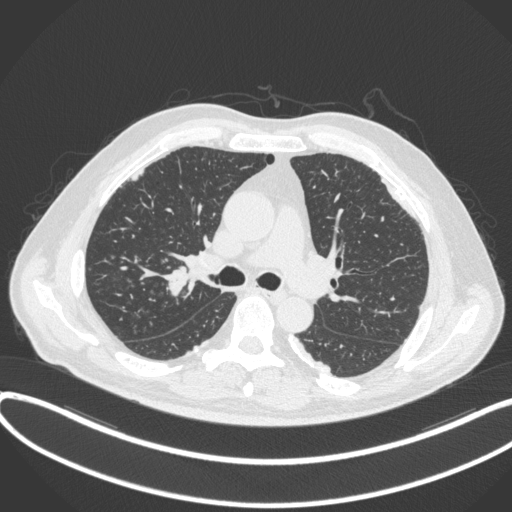
Chest CT, one axial slice. Reconstruction kernel B31f. 120 kVp. Lung window (W 1500 / L -600 HU). 1 mm slice thickness. 512 × 512 image matrix. Male patient, age 58 years. Case-level facts recorded for this patient, not image findings: clinical TNM (as recorded): T1c N0 M0.
Annotated regions visible in this slice (bounding box drawn by a radiologist):
- lung tumour (recorded histology: squamous cell carcinoma): bounding box (x1, y1, x2, y2) in pixels: (160, 261, 191, 296)